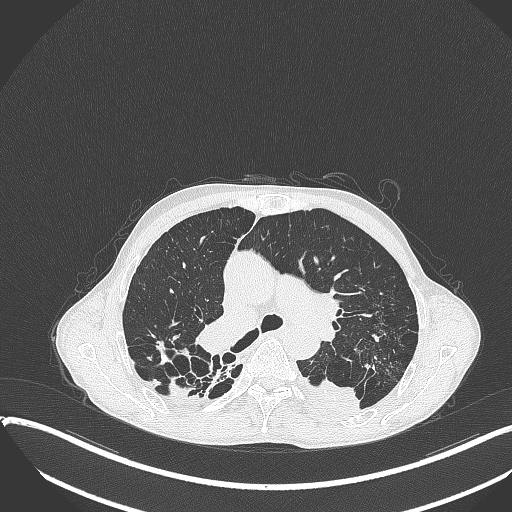
Chest CT, one axial slice; slice 249 of 401 in the series (ordered by position); reconstruction kernel B70f; lung window (W 1500 / L -600 HU); 1 mm slice thickness; 512 × 512 image matrix. Male patient, age 57 years. From the clinical record (not read from this slice): clinical TNM (as recorded): T4 N0 M0.
Annotated regions visible in this slice (bounding box drawn by a radiologist):
- lung tumour (recorded histology: squamous cell carcinoma): box from (x=297, y=371) to (x=367, y=421) px